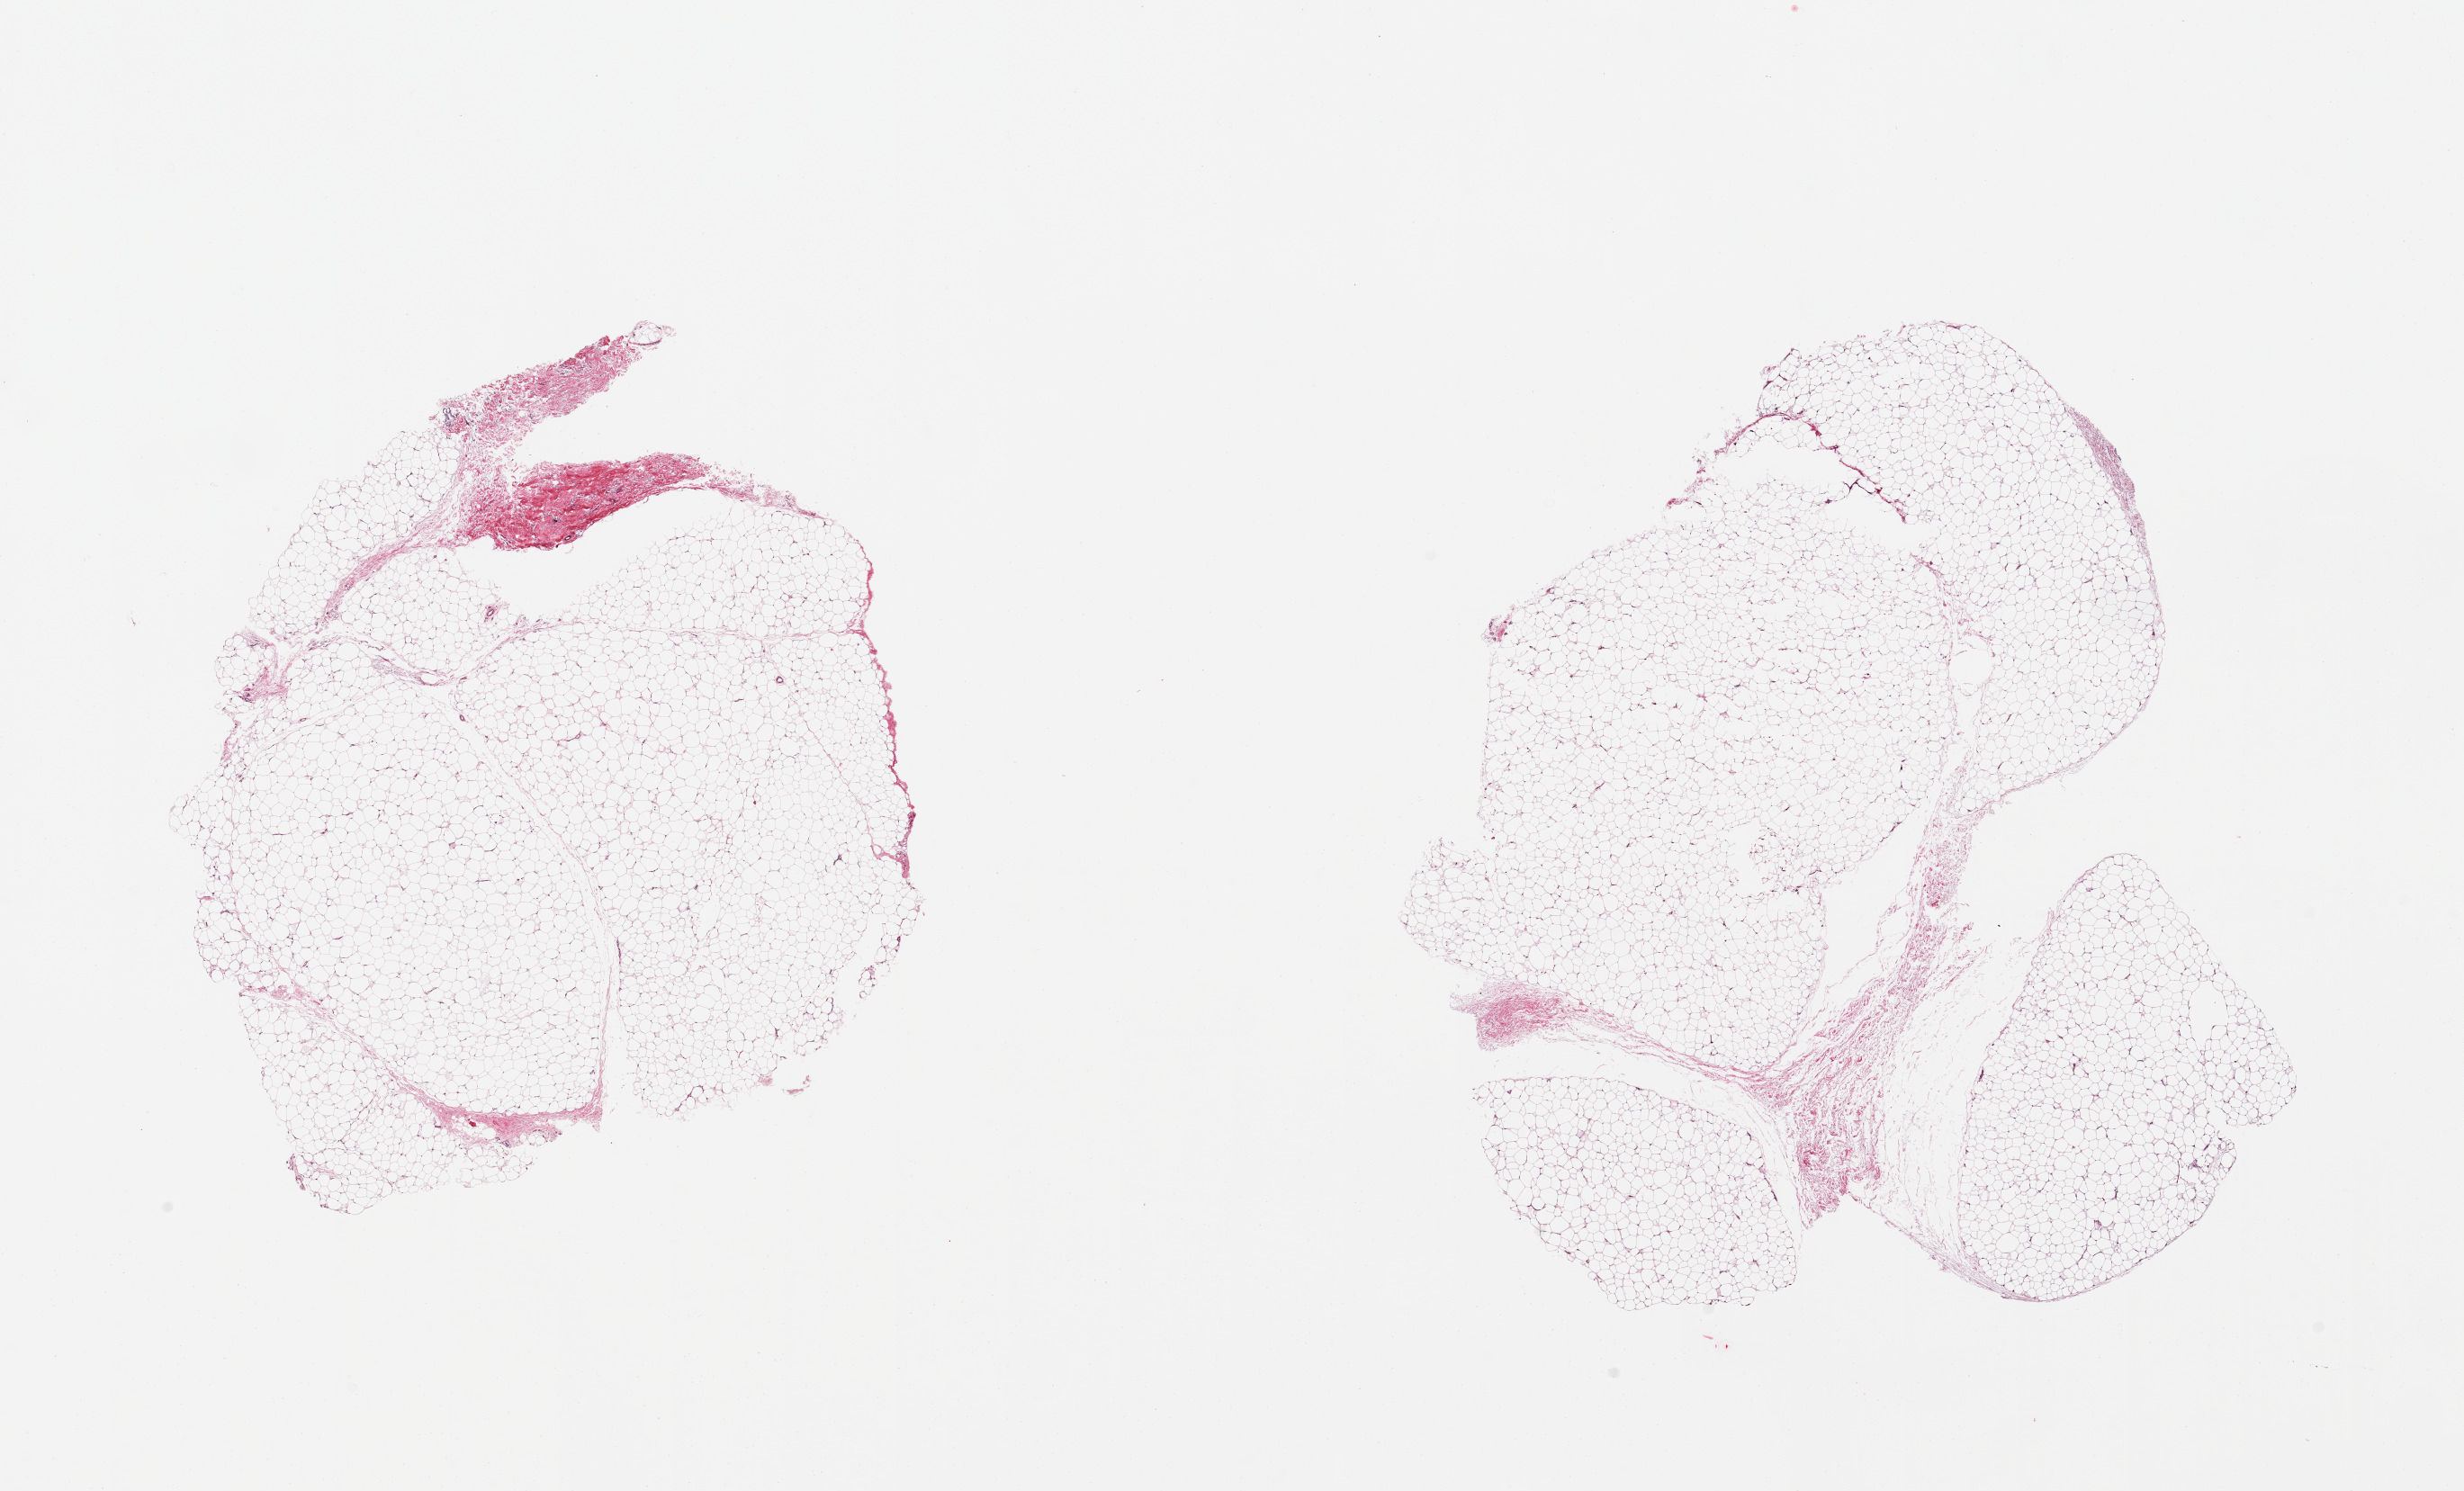
Hematoxylin and eosin (H&E) whole-slide image — whole scanned area (about 21.7 x 13.1 mm, from a 20x scan) shown as a low-resolution overview, PAXgene-fixed paraffin-embedded (PFPE) section, section of adipose tissue (target tissue), tissue donor sample.
Reviewer comment on this tissue sample: 2 pieces; <5% fibrous content.